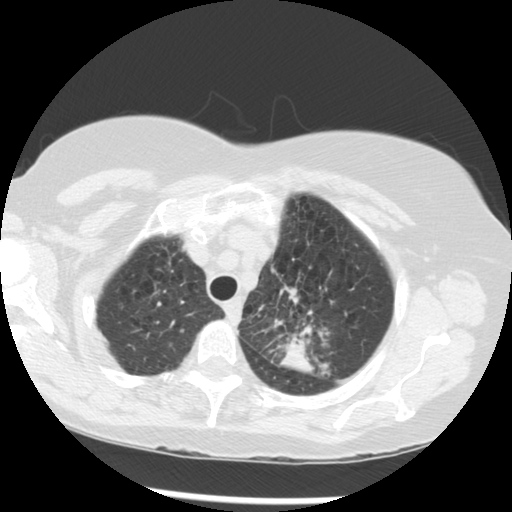
Low-dose screening chest CT, one axial slice. Position 234 of 283 along the scan axis. Reconstruction kernel STANDARD. Lung window (W 1500 / L -600 HU). 2.5 mm slice thickness. 512 × 512 image matrix.
Annotated regions visible in this slice (outlined manually by an expert reader):
- lesion 1 (tumor, upper lobe of left lung): bounding box (x1, y1, x2, y2) in pixels: (279, 287, 316, 376)